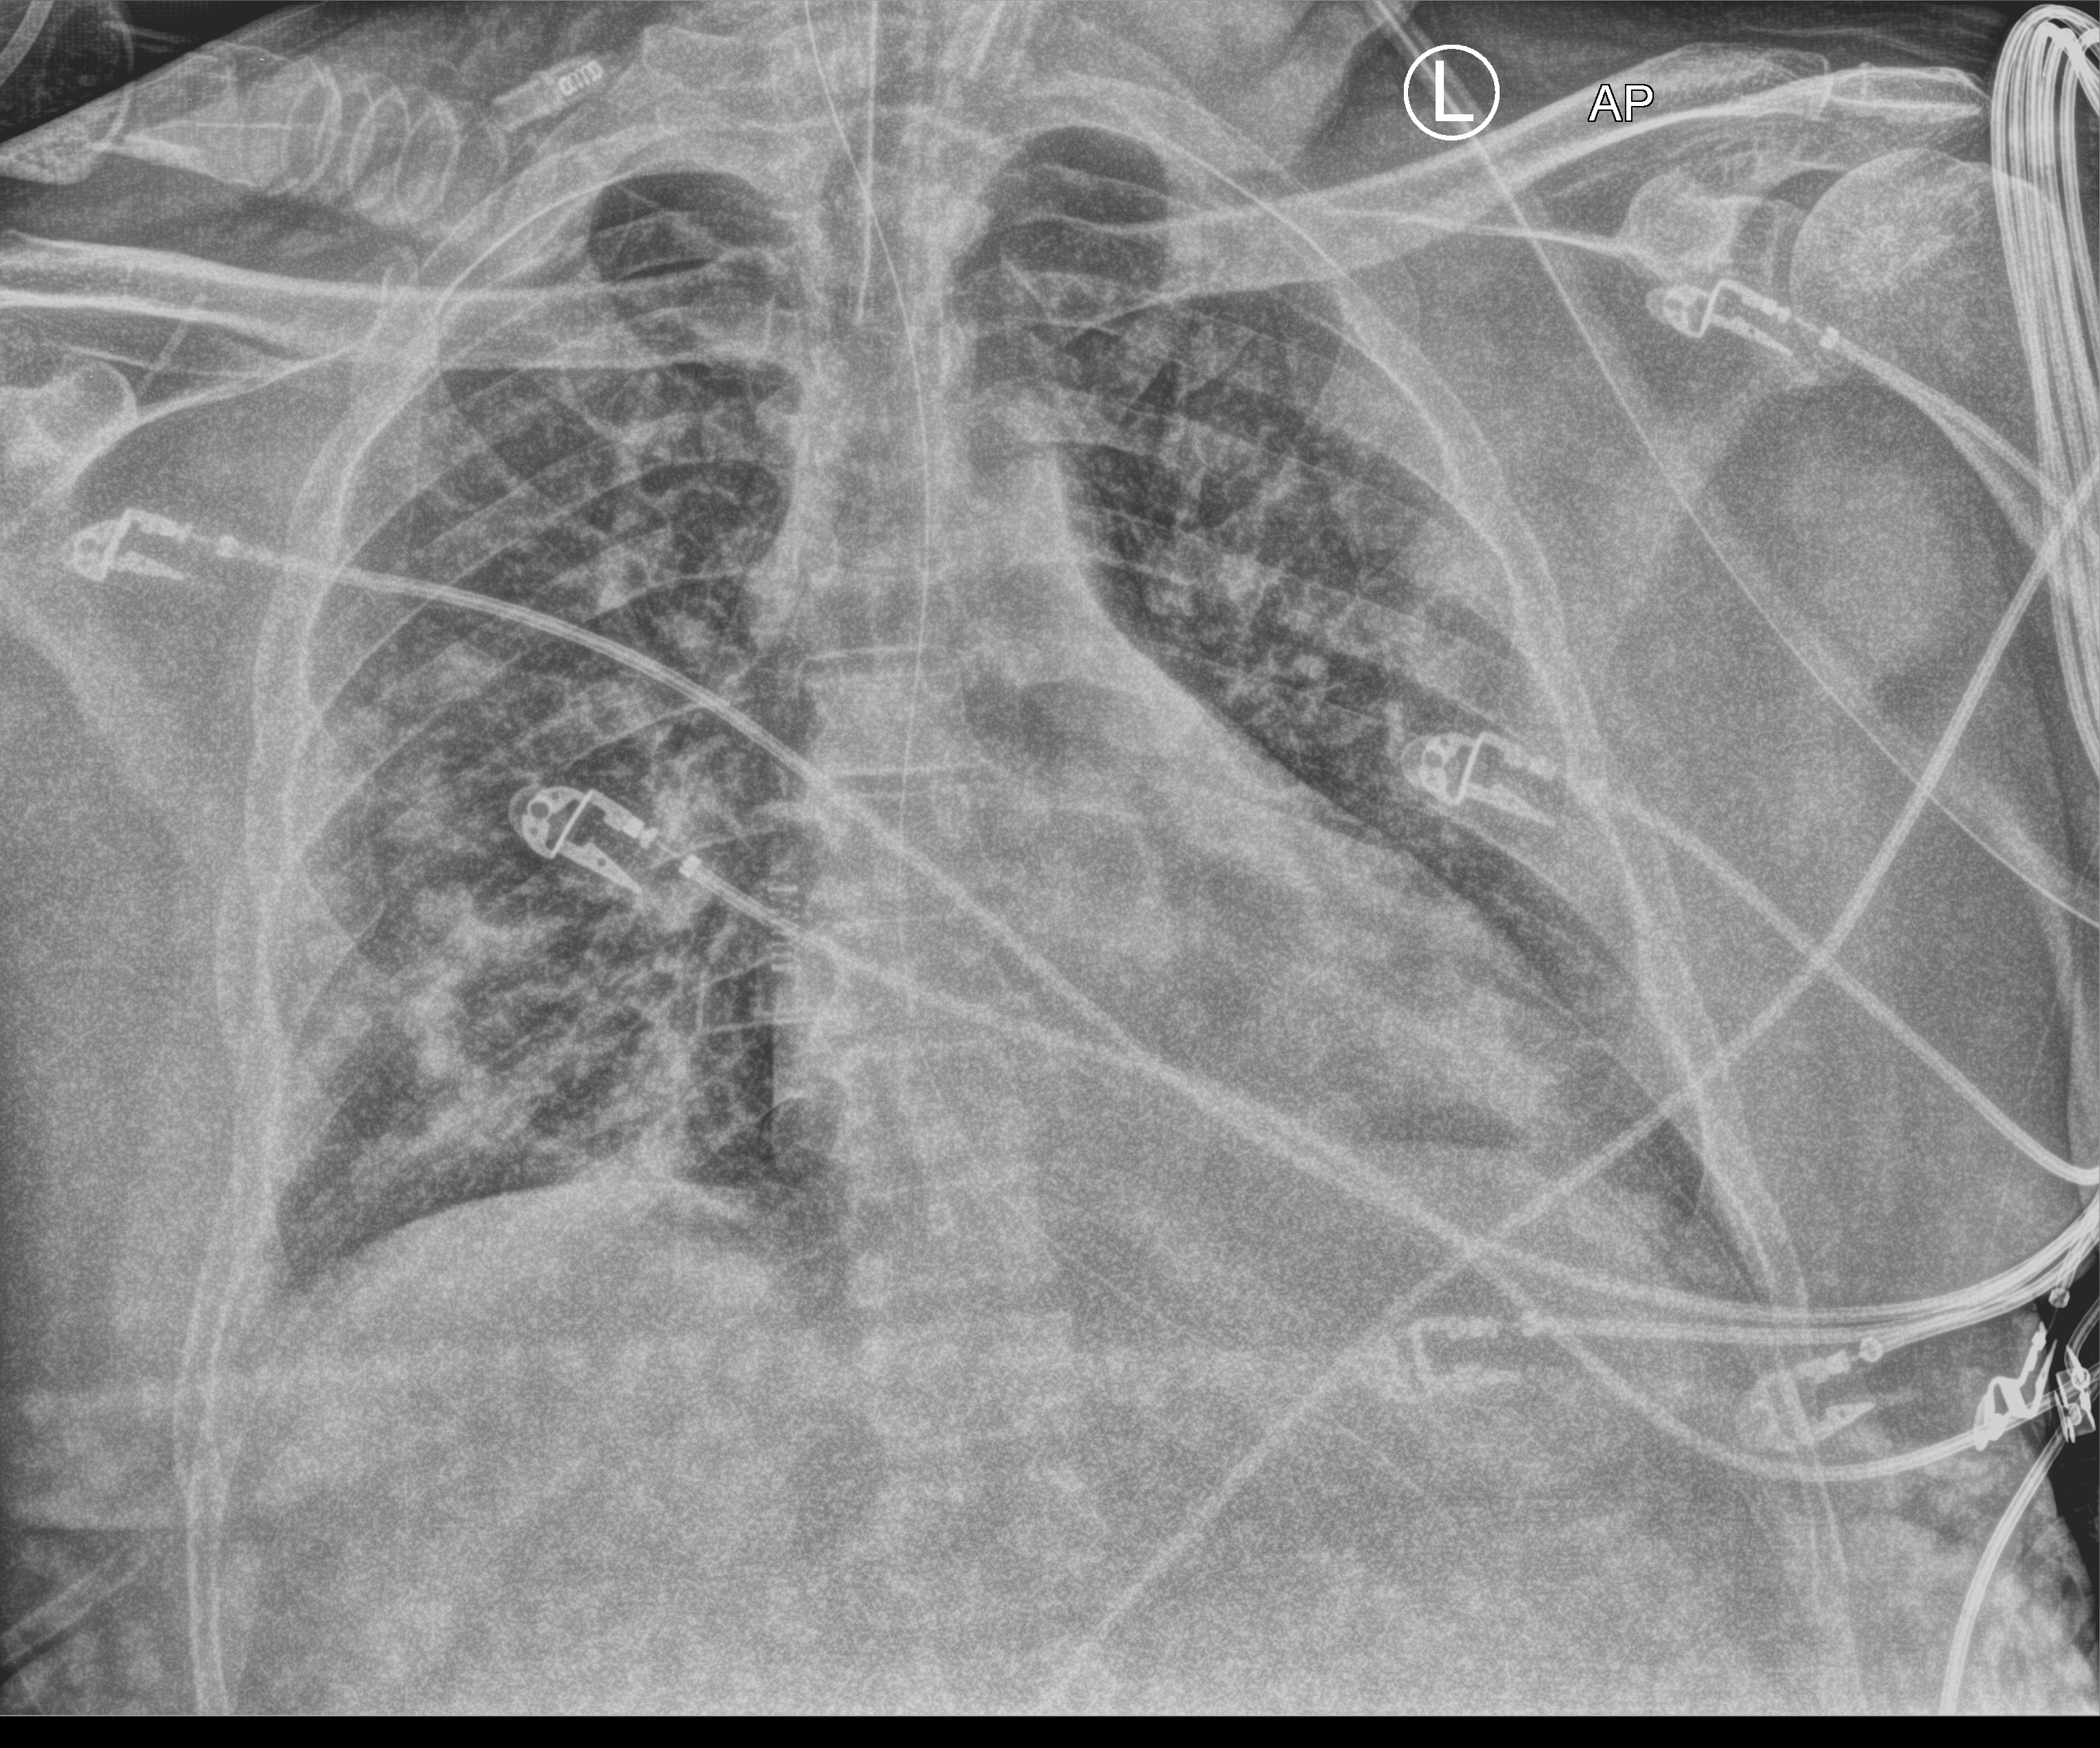
Bedside chest radiograph (computed radiography). Patient hospitalised with COVID-19; male, aged 18–59 years.
From the hospital-stay record, not from the radiograph (when in the stay this image was taken is not recorded): chronic kidney disease (admission record): no.